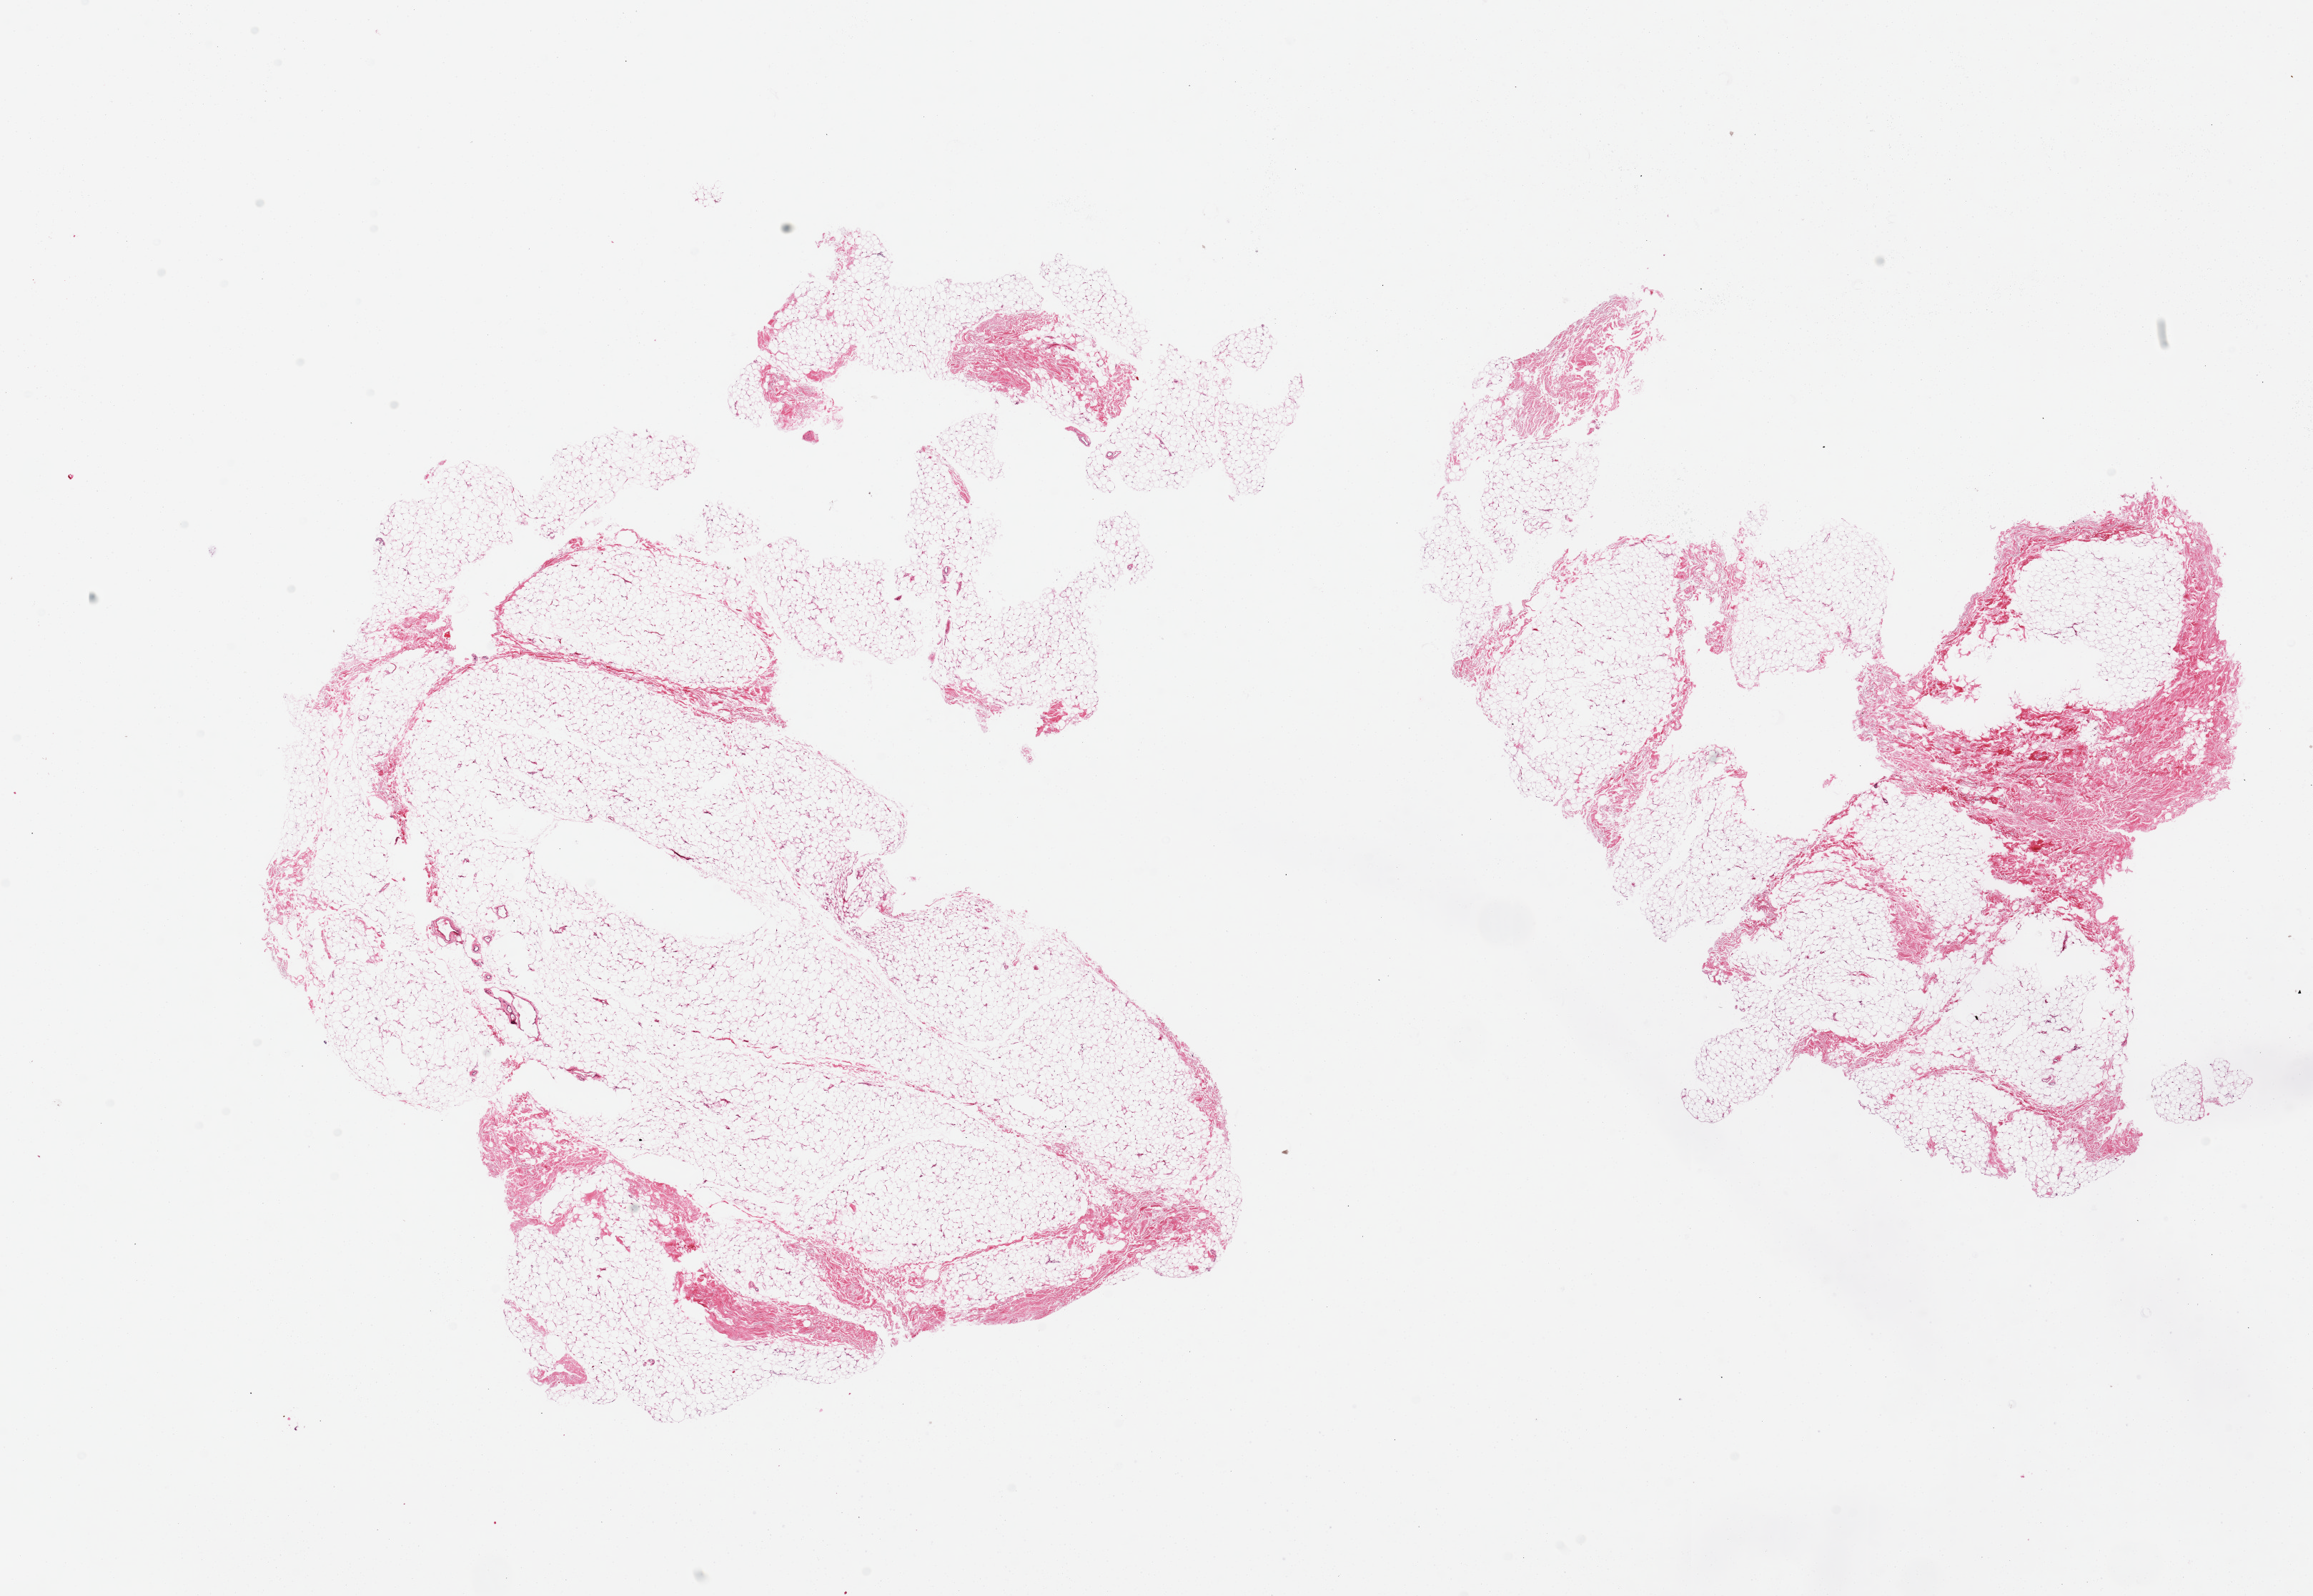
Digitized haematoxylin and eosin-stained section — low-resolution overview of the scanned area, about 25.6 x 17.7 mm. PAXgene-fixed, paraffin-embedded tissue. Section of breast (target tissue). Donor tissue sample.
- reviewer comment on this tissue sample: 2 pieces; mature adipose tissue with fibrovascular component; no evidence of ductal structures